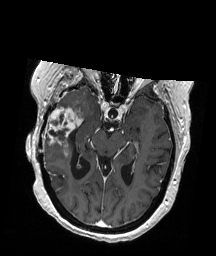
Brain MRI from a brain-tumour surgery series, one axial slice; T1-weighted post-contrast; 1 mm slice thickness; 216 × 256 image matrix, field of view 211 × 250 mm. From the clinical record (not read from this slice): histopathology: Glioblastoma; WHO grade: 4; IDH mutation: no; tumour location: Right Temporal.
Outlined on this slice (outlined manually by an expert reader):
- tumour: bounding box <42,105,83,156> (left, top, right, bottom; pixels)